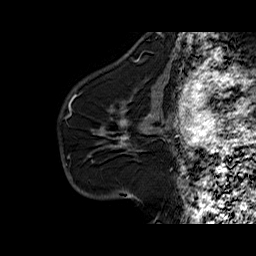
Breast MRI (dynamic contrast-enhanced), one sagittal slice. Position 40 of 60 along the scan axis. Dynamic contrast-enhanced series, time point 2 of 6 at this slice position (early post-contrast). 1.5 T. TE 6.3 ms, TR 32.5 ms. 256 × 256 image matrix. Female patient. Case-level facts recorded for this patient, not image findings: setting: breast cancer imaged before/during neoadjuvant chemotherapy; receptor status: HR-positive, HER2-negative.
Outlined on this slice (semi-automatically segmented with operator editing):
- analysis volume of interest (the breast-tissue region the enhancement analysis was run in; not a lesion): bounding box [x1, y1, x2, y2] px = [94, 103, 161, 163]
- tumour enhancement mask (voxels above the 100 % enhancement threshold inside the analysis volume of interest): [120, 120, 128, 145]